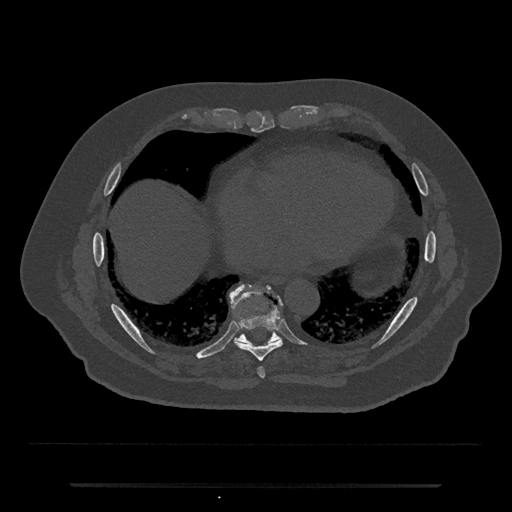
CT including the spine, one axial slice. Position 792 of 797 along the scan axis. Reconstruction kernel Br40s/3. 120 kVp. Bone window (W 1800 / L 400 HU). 512 × 512 image matrix. Patient: male, 80 years. Case-level facts recorded for this patient, not image findings: primary cancer: prostate; vertebrae with lytic lesions (as recorded): L1, T11.
Annotated regions visible in this slice (semi-automatically segmented with operator editing):
- T8 vertebra: bounding box (x1, y1, x2, y2) in pixels: (235, 308, 282, 361)
- T9 vertebra: (230, 284, 281, 347)